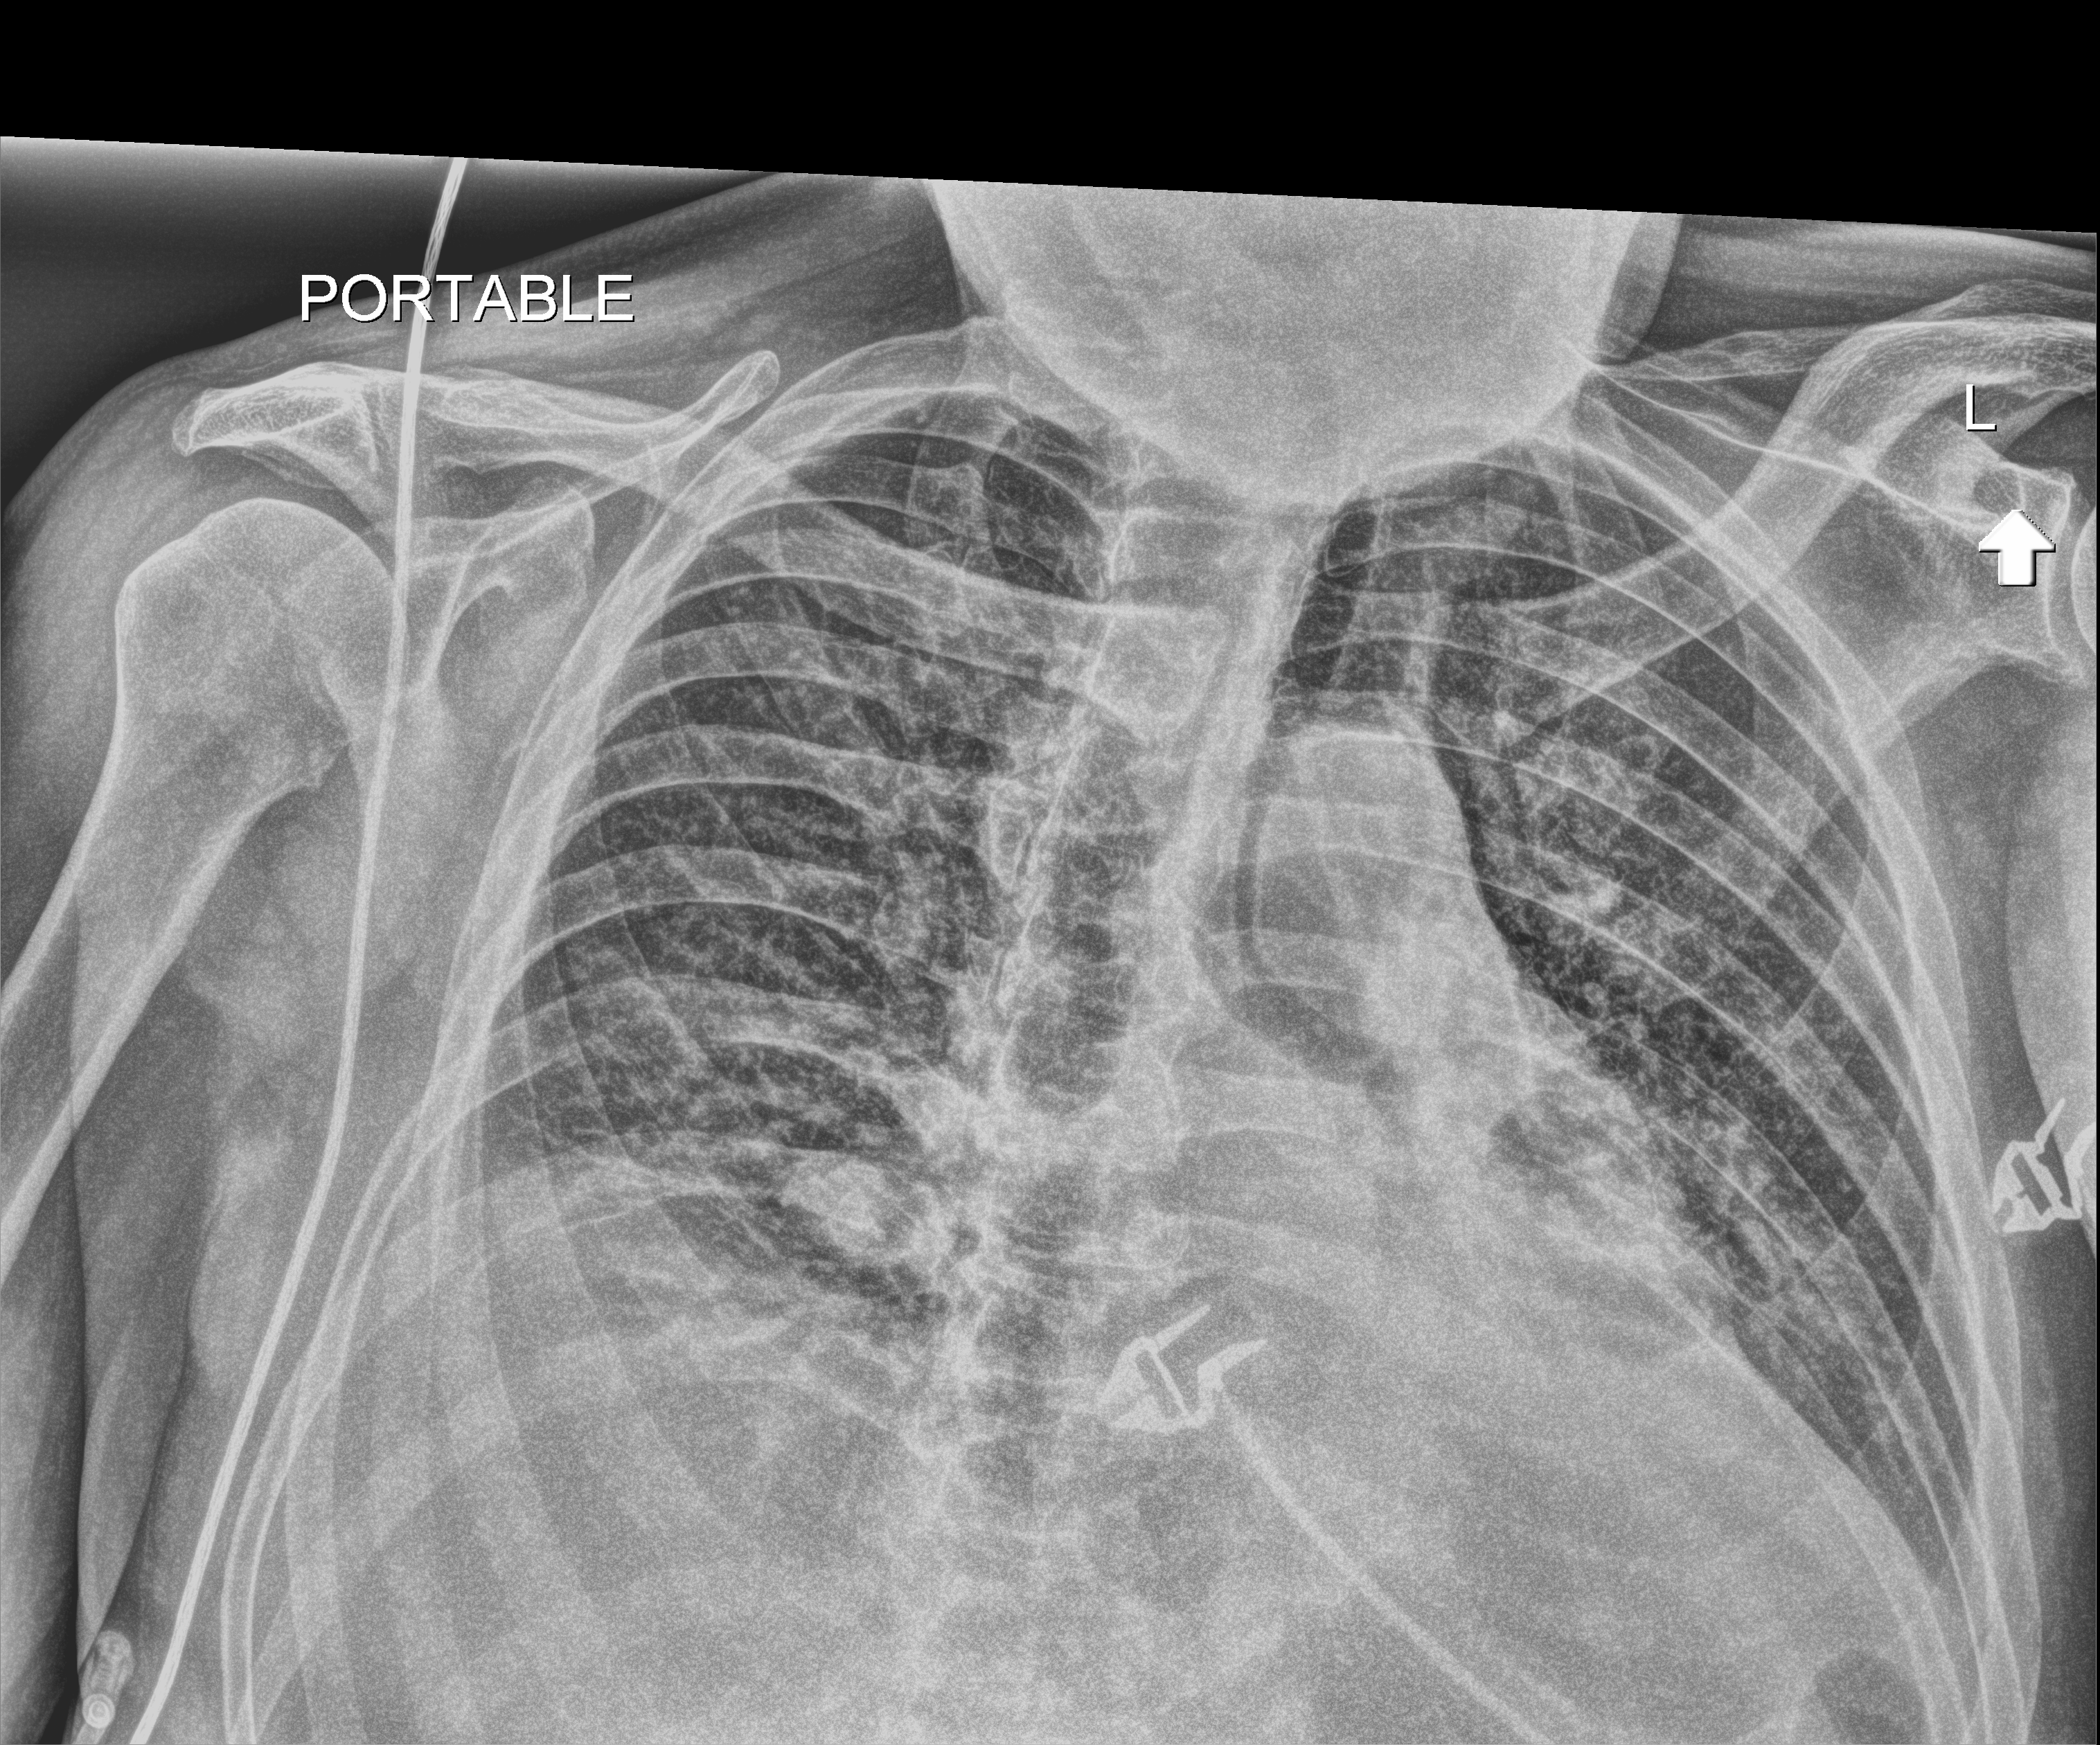
Chest radiograph (digital radiography); anteroposterior (AP) projection. Male patient hospitalised with COVID-19, age 18–59 years.
Hospital-stay facts (about this admission, not read from this image; timing relative to this image not recorded): admitted to intensive care during this hospital stay: no.